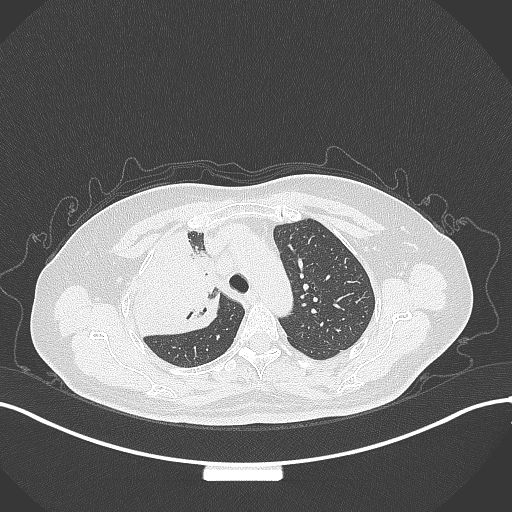
Chest CT, one axial slice; slice 236 of 309 in the series (ordered by position); reconstruction kernel B70f; 120 kVp; lung window (W 1500 / L -600 HU); 1 mm slice thickness; 512 × 512 image matrix. Female patient, age 60 years. From the clinical record (not read from this slice): clinical TNM (as recorded): T3 N1 M1.
Annotated regions visible in this slice (rectangle marked by the reading radiologist):
- lung tumour (recorded histology: adenocarcinoma): bounding box (x1, y1, x2, y2) in pixels: (123, 224, 223, 343)